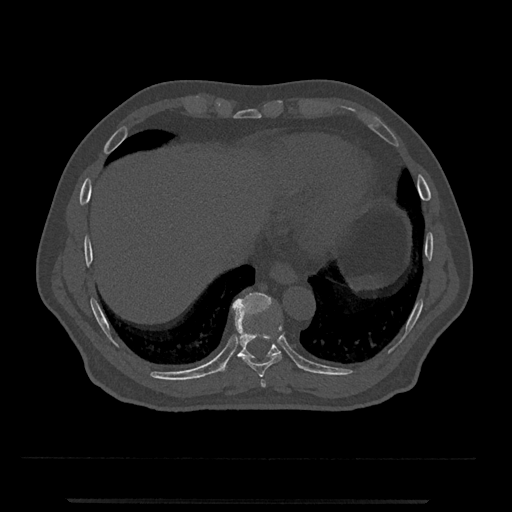
CT including the spine, one axial slice; position 548 of 797 along the scan axis; reconstruction kernel Br40s/3; bone window (W 1800 / L 400 HU); 512 × 512 image matrix. Male patient, age 63 years. Case-level facts recorded for this patient, not image findings: primary cancer: prostate.
Outlined on this slice (semi-automatic segmentation, software-assisted and operator-edited):
- T10 vertebra: bounding box <218,292,281,373> (left, top, right, bottom; pixels)
- T8 vertebra: <260,379,266,387>
- T9 vertebra: <243,326,282,377>